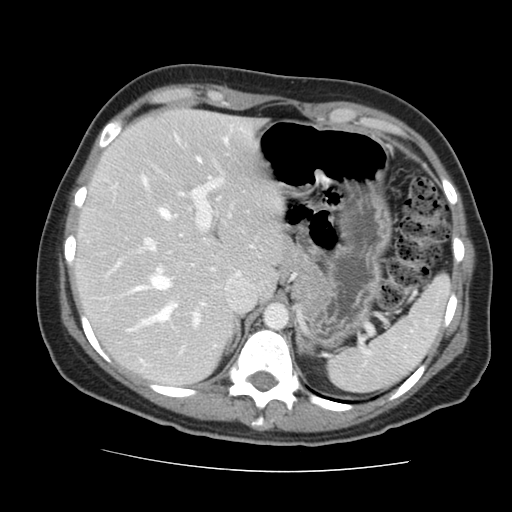
Contrast-enhanced abdominal CT, one axial slice. Slice 106 of 144 in the series (ordered by position). 120 kVp. Intravenous contrast given. Soft-tissue window (W 400 / L 40 HU). 512 × 512 image matrix, field of view 333 × 333 mm. Female patient, age 46 years. Case-level facts recorded for this patient, not image findings: diagnosis: colorectal cancer liver metastases, imaged before liver resection; multiple liver metastases: no; largest metastasis: 2.8 cm; disease in both lobes: no.
Structures marked on this image (outlined manually by an expert reader):
- hepatic veins: bounding box [x1, y1, x2, y2] px = [134, 178, 177, 318]
- liver: [78, 110, 281, 384]
- planned liver remnant (the part of the liver to remain after resection): [78, 110, 281, 384]
- portal vein (with intrahepatic branches): [110, 179, 232, 332]